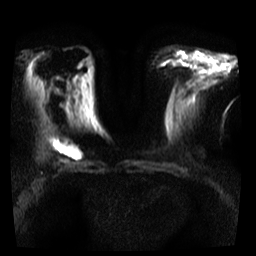
Breast MRI, one axial slice. Position 13 of 35 along the scan axis. Diffusion-weighted series; image 2 of 4 stored at this slice position (different b-values; order by instance number). 3 T. 256 × 256 image matrix, field of view 300 × 300 mm. Female patient.
Annotated regions visible in this slice (outlined manually by an expert reader):
- tumour on diffusion-weighted imaging: bounding box <47,135,83,160> (left, top, right, bottom; pixels)